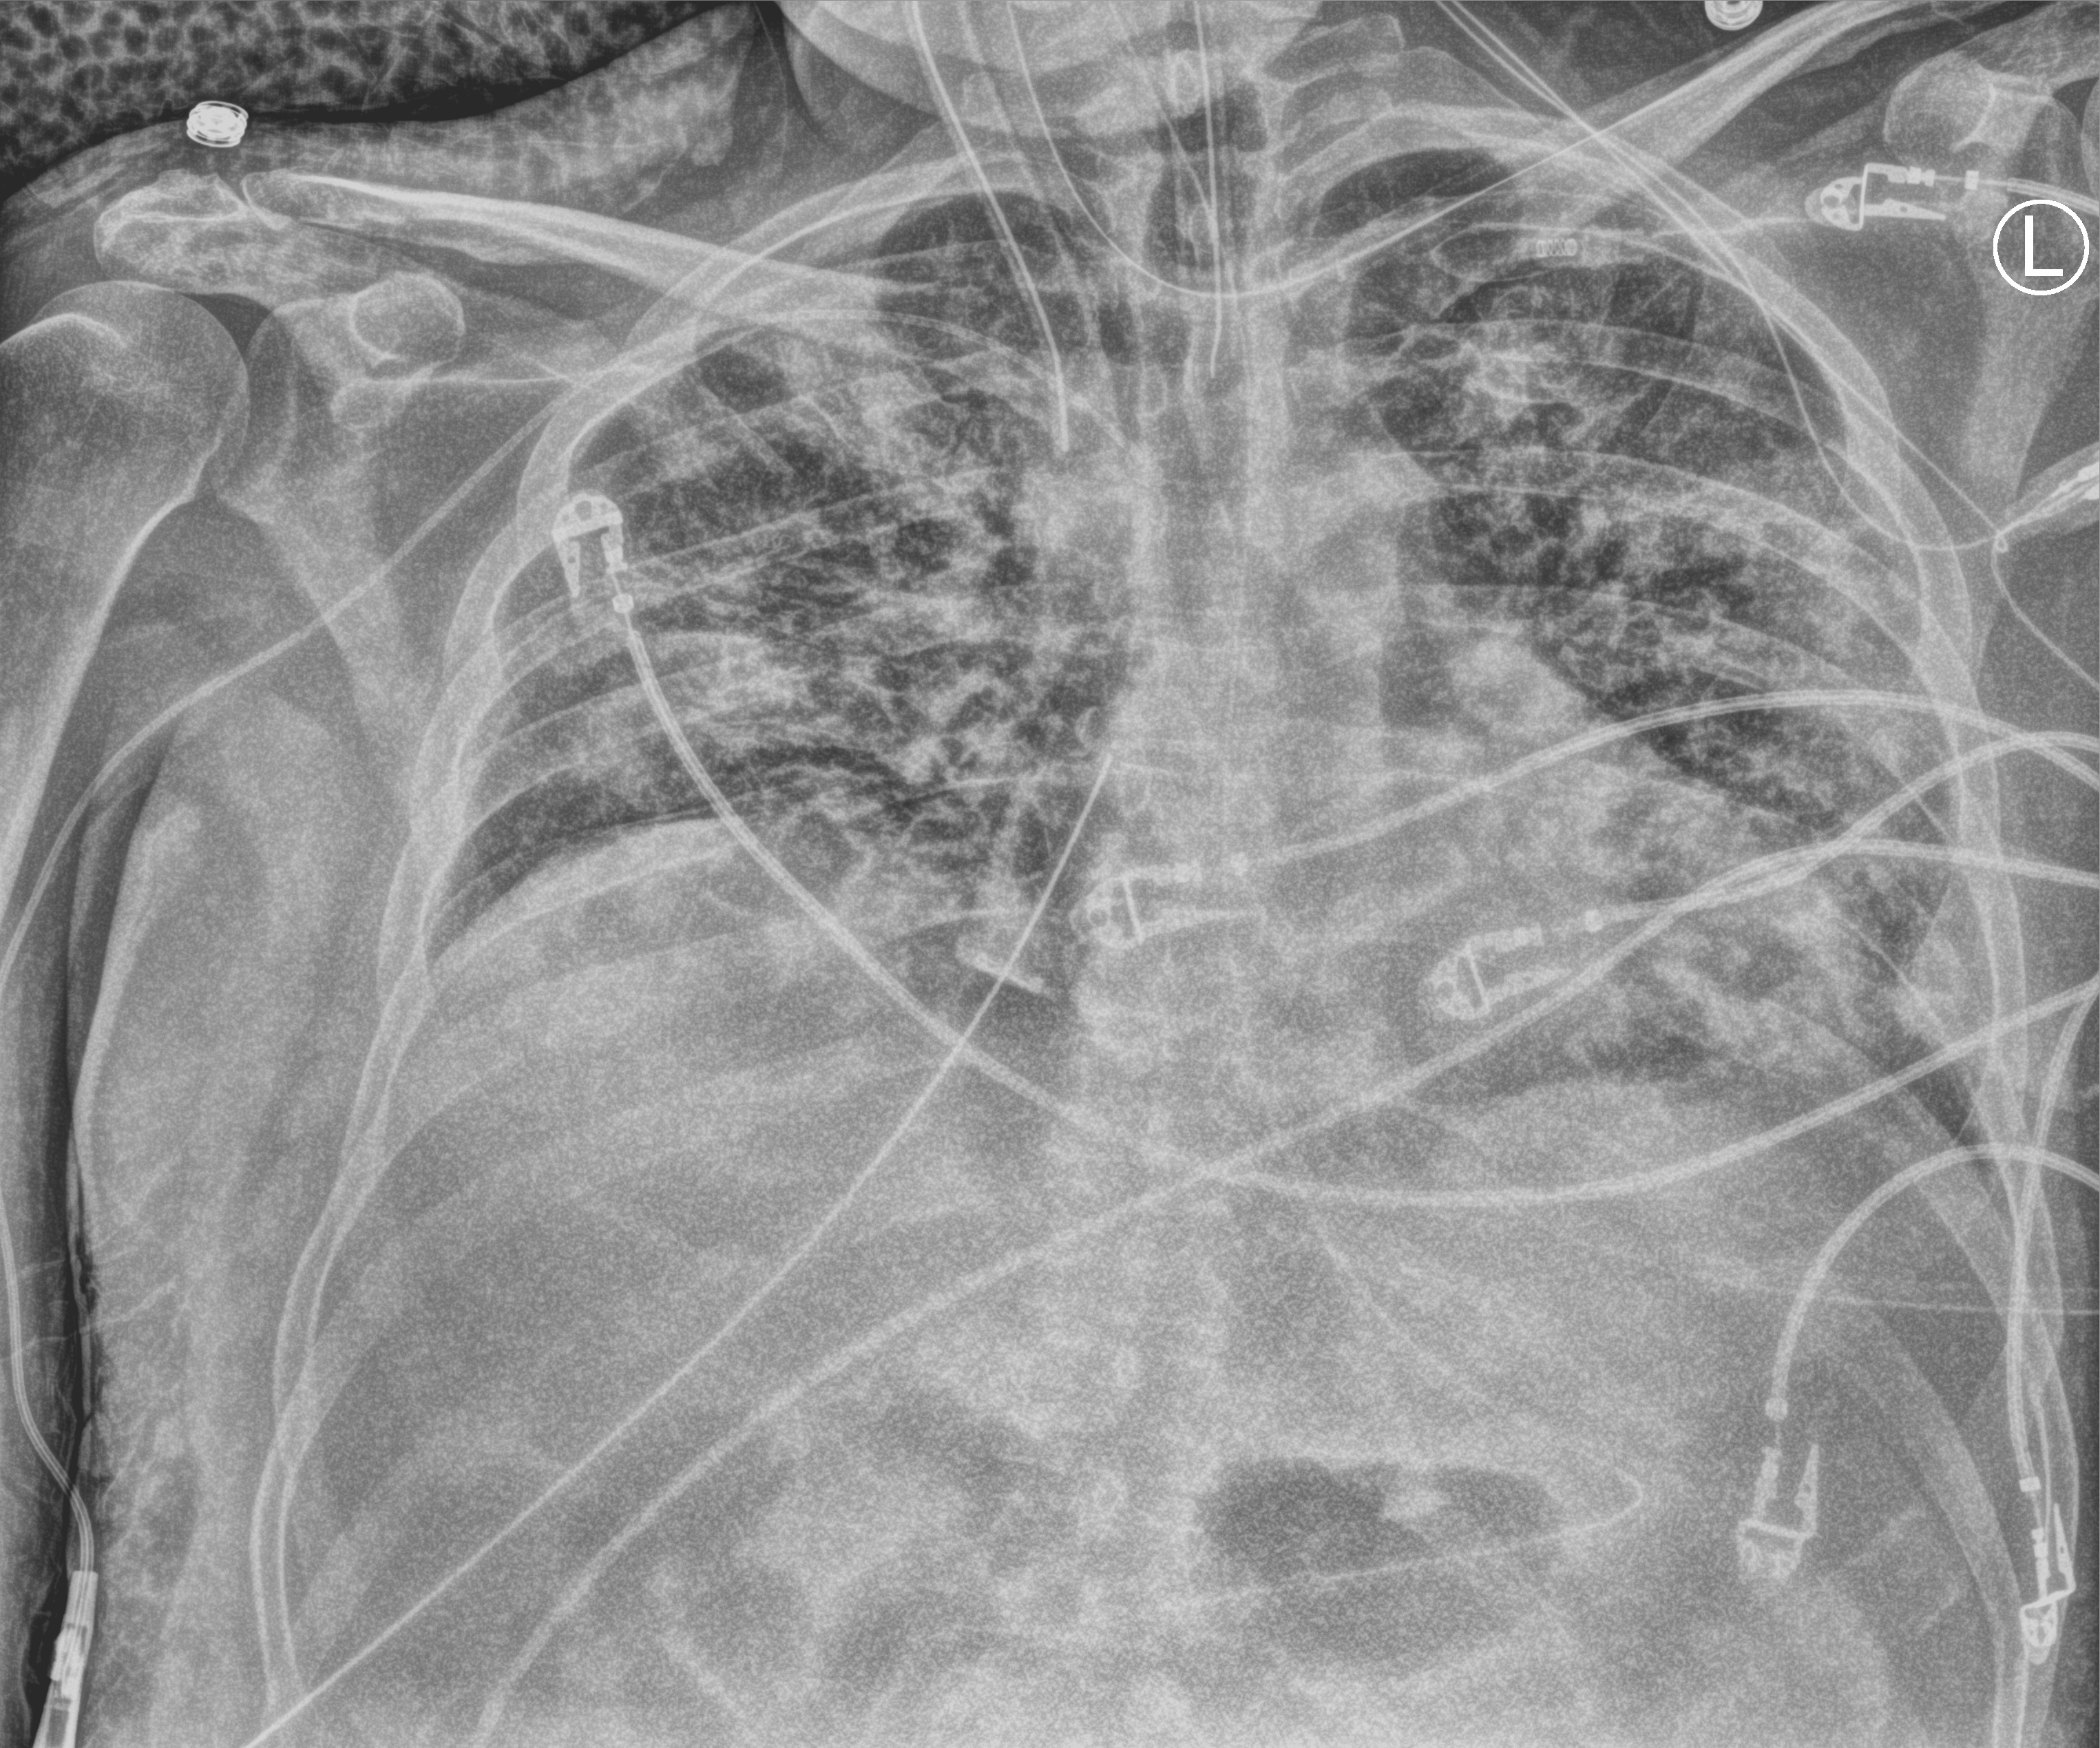
Chest X-ray (portable); anteroposterior (AP) projection. Male patient hospitalised with COVID-19, age 18–59 years.
Admission-level facts for this patient (not findings on this image; timing relative to this image not recorded): diabetes (admission record): no.